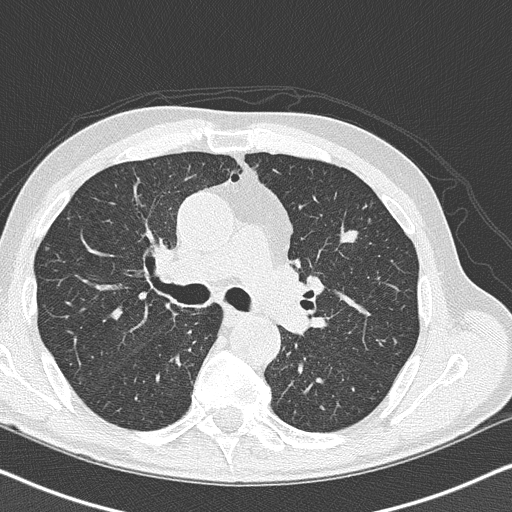
Chest CT (low-dose screening protocol), one axial image. Second screening round (one year after baseline). Lung window (W 1500 / L -600 HU). 2 mm slice thickness. 512 × 512 image matrix. Male participant, aged 73 years at enrolment.
Lesion marked by an expert reader, box from (x=317, y=219) to (x=377, y=269) px. The screening reader recorded 3 non-calcified nodules or masses ≥4 mm on this exam (left upper lobe, left upper lobe, right lower lobe); which of them this box marks is not recorded. Official screen result: positive, other. Later outcome: lung cancer diagnosed 36 days after this screen — small cell carcinoma, NOS, left upper lobe, stage IIIB (AJCC 6th edition), 19 mm at pathology.